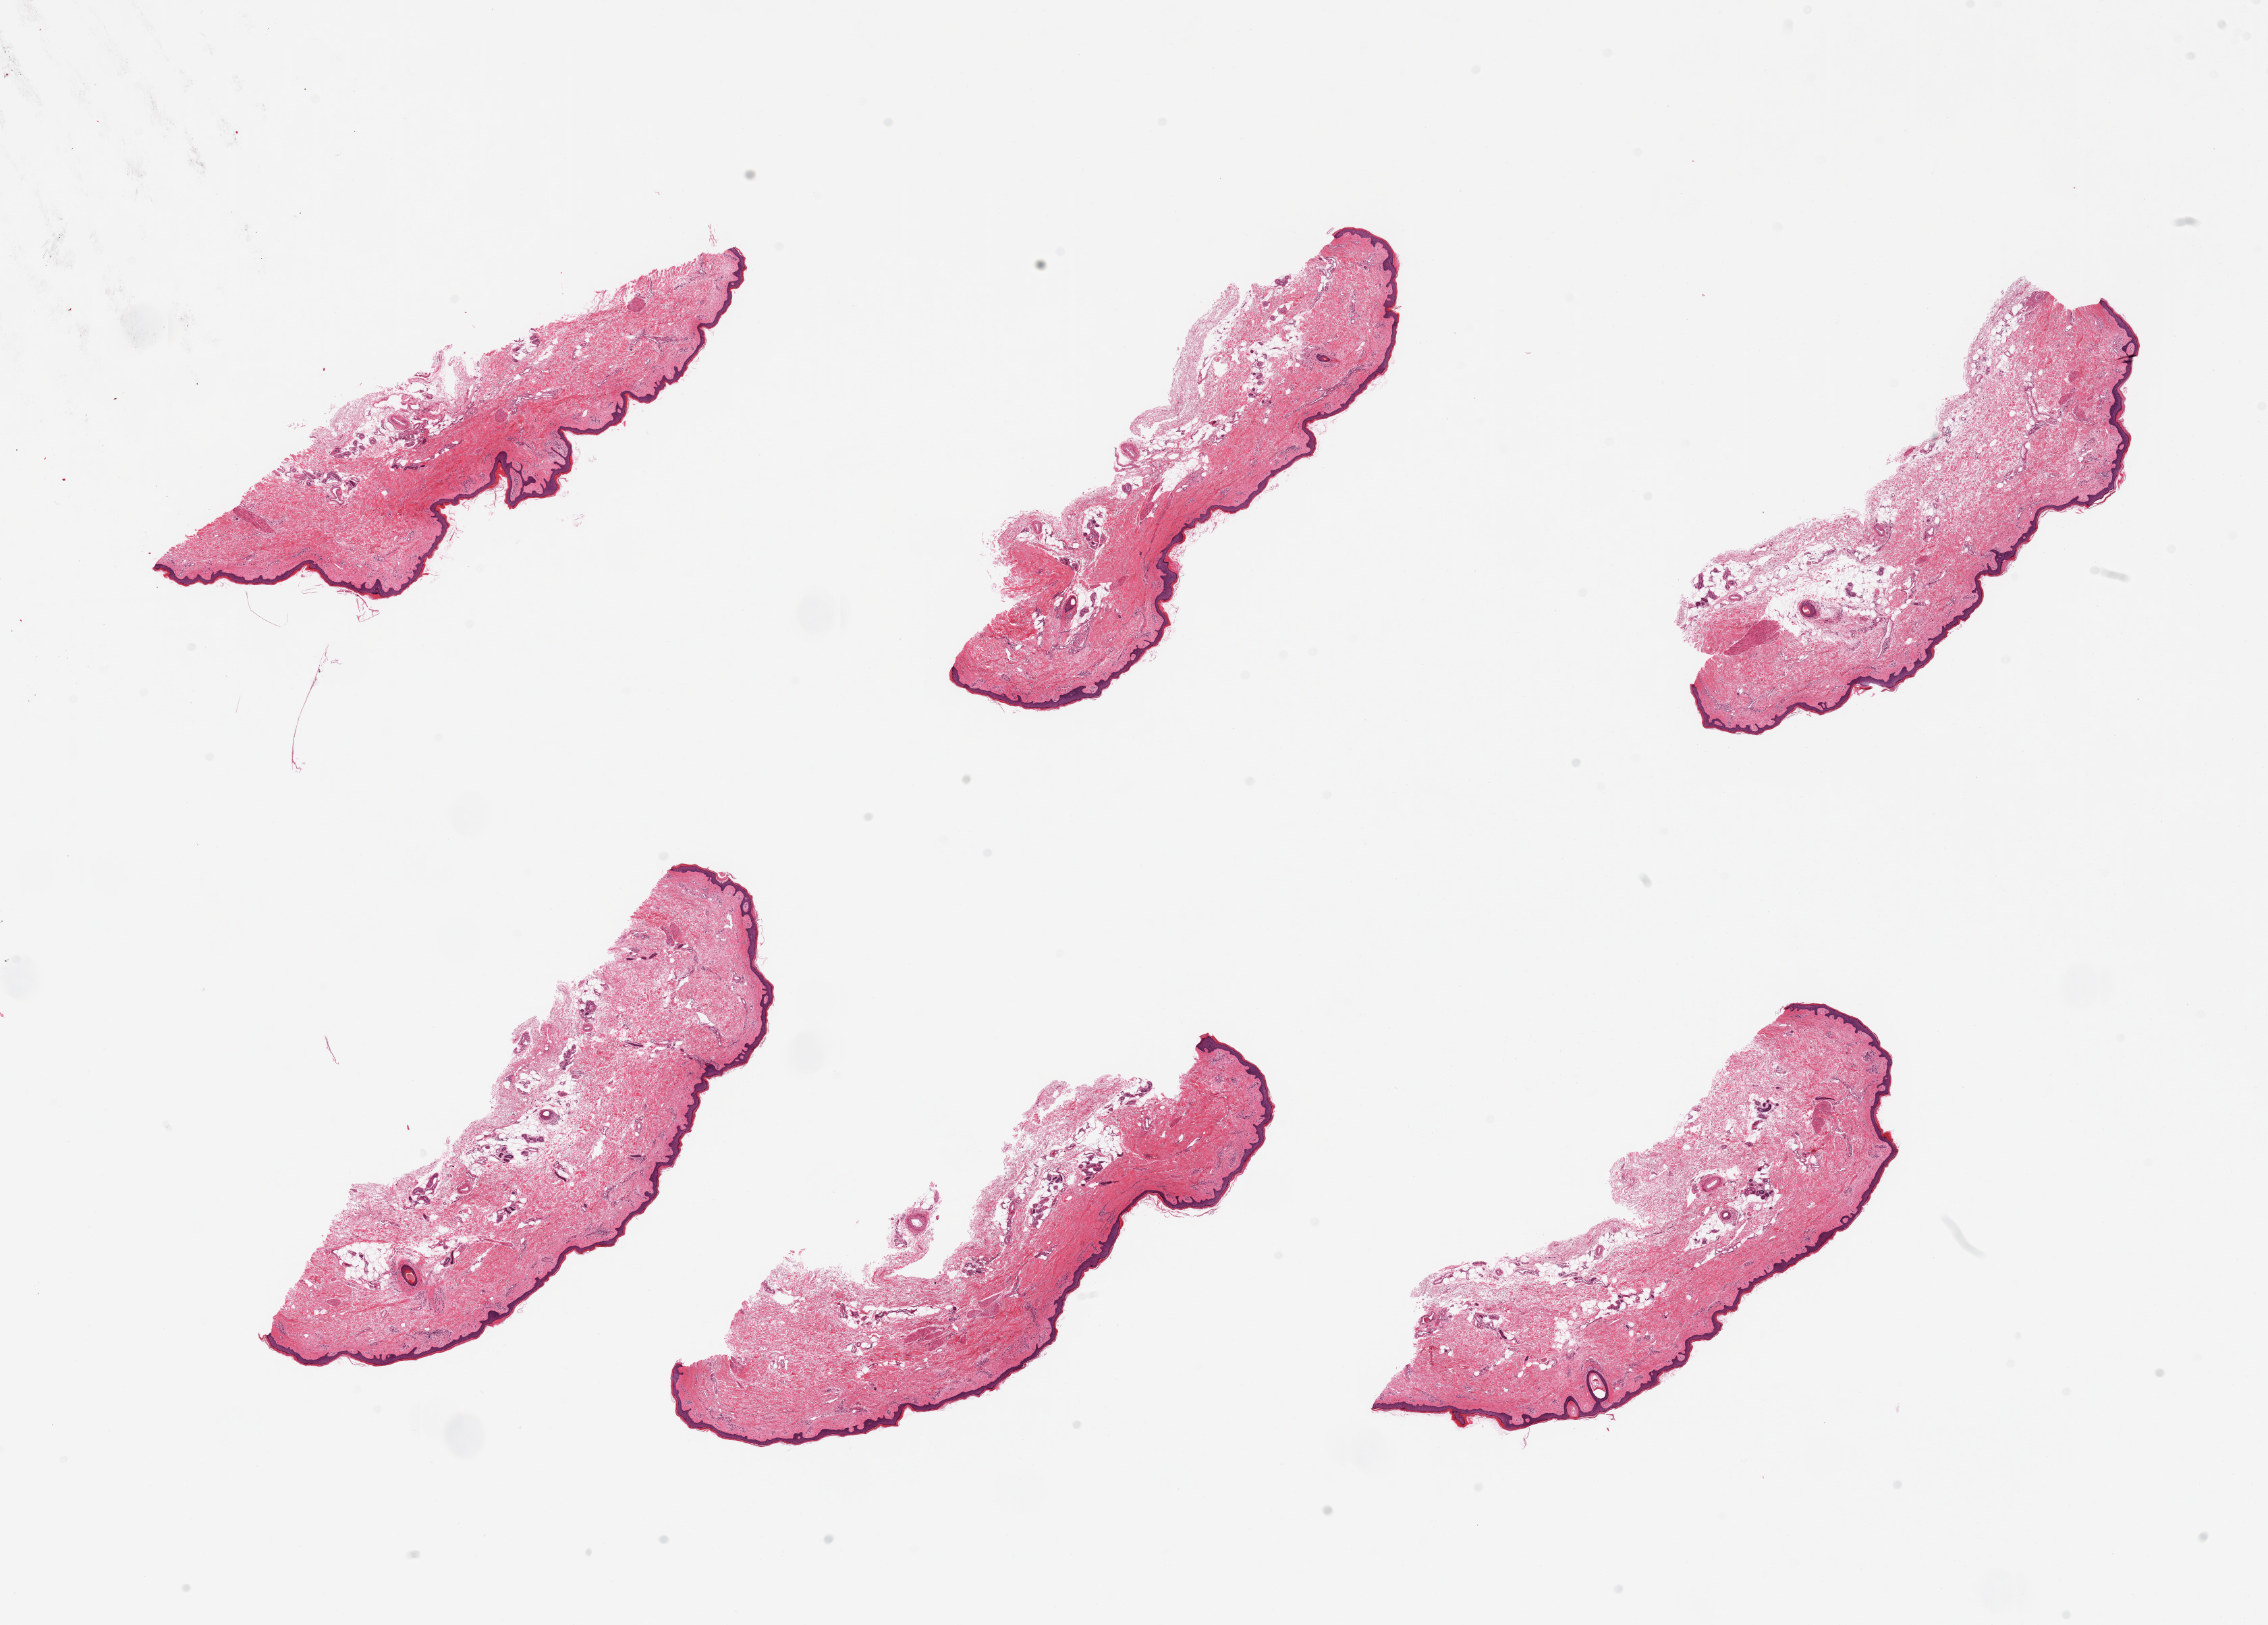
H&E whole-slide image, brightfield — a low-resolution overview of the entire scanned area, about 26.6 x 19.0 mm (acquisition: 20x scan), PAXgene-fixed paraffin-embedded (PFPE) section, target tissue: skin of lower leg, donor tissue sample. Donor sex: female.
* pathologist's review note for this sample: 6 pieces; well trimmed; <10% intradermal fat